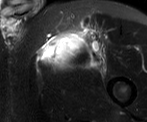
MRI of an extremity soft-tissue mass, one axial slice. Position 51 of 52 along the scan axis. T2-weighted fat-saturated. MR volume resampled by the dataset authors to the PET/CT grid (not the native acquisition matrix). 3.27 mm slice thickness. 147 × 122 image matrix, field of view 144 × 119 mm. Male patient. Case-level facts recorded for this patient, not image findings: histological type: pleiomorphic liposarcoma; grade: high; site of the primary tumour: left thigh.
Annotated regions visible in this slice (expert contour drawn on MRI and transferred to this co-registered scan by the dataset authors):
- gross tumour volume including surrounding oedema: bounding box (x1, y1, x2, y2) in pixels: (41, 27, 104, 65)
- gross tumour volume (mass): (41, 34, 79, 63)